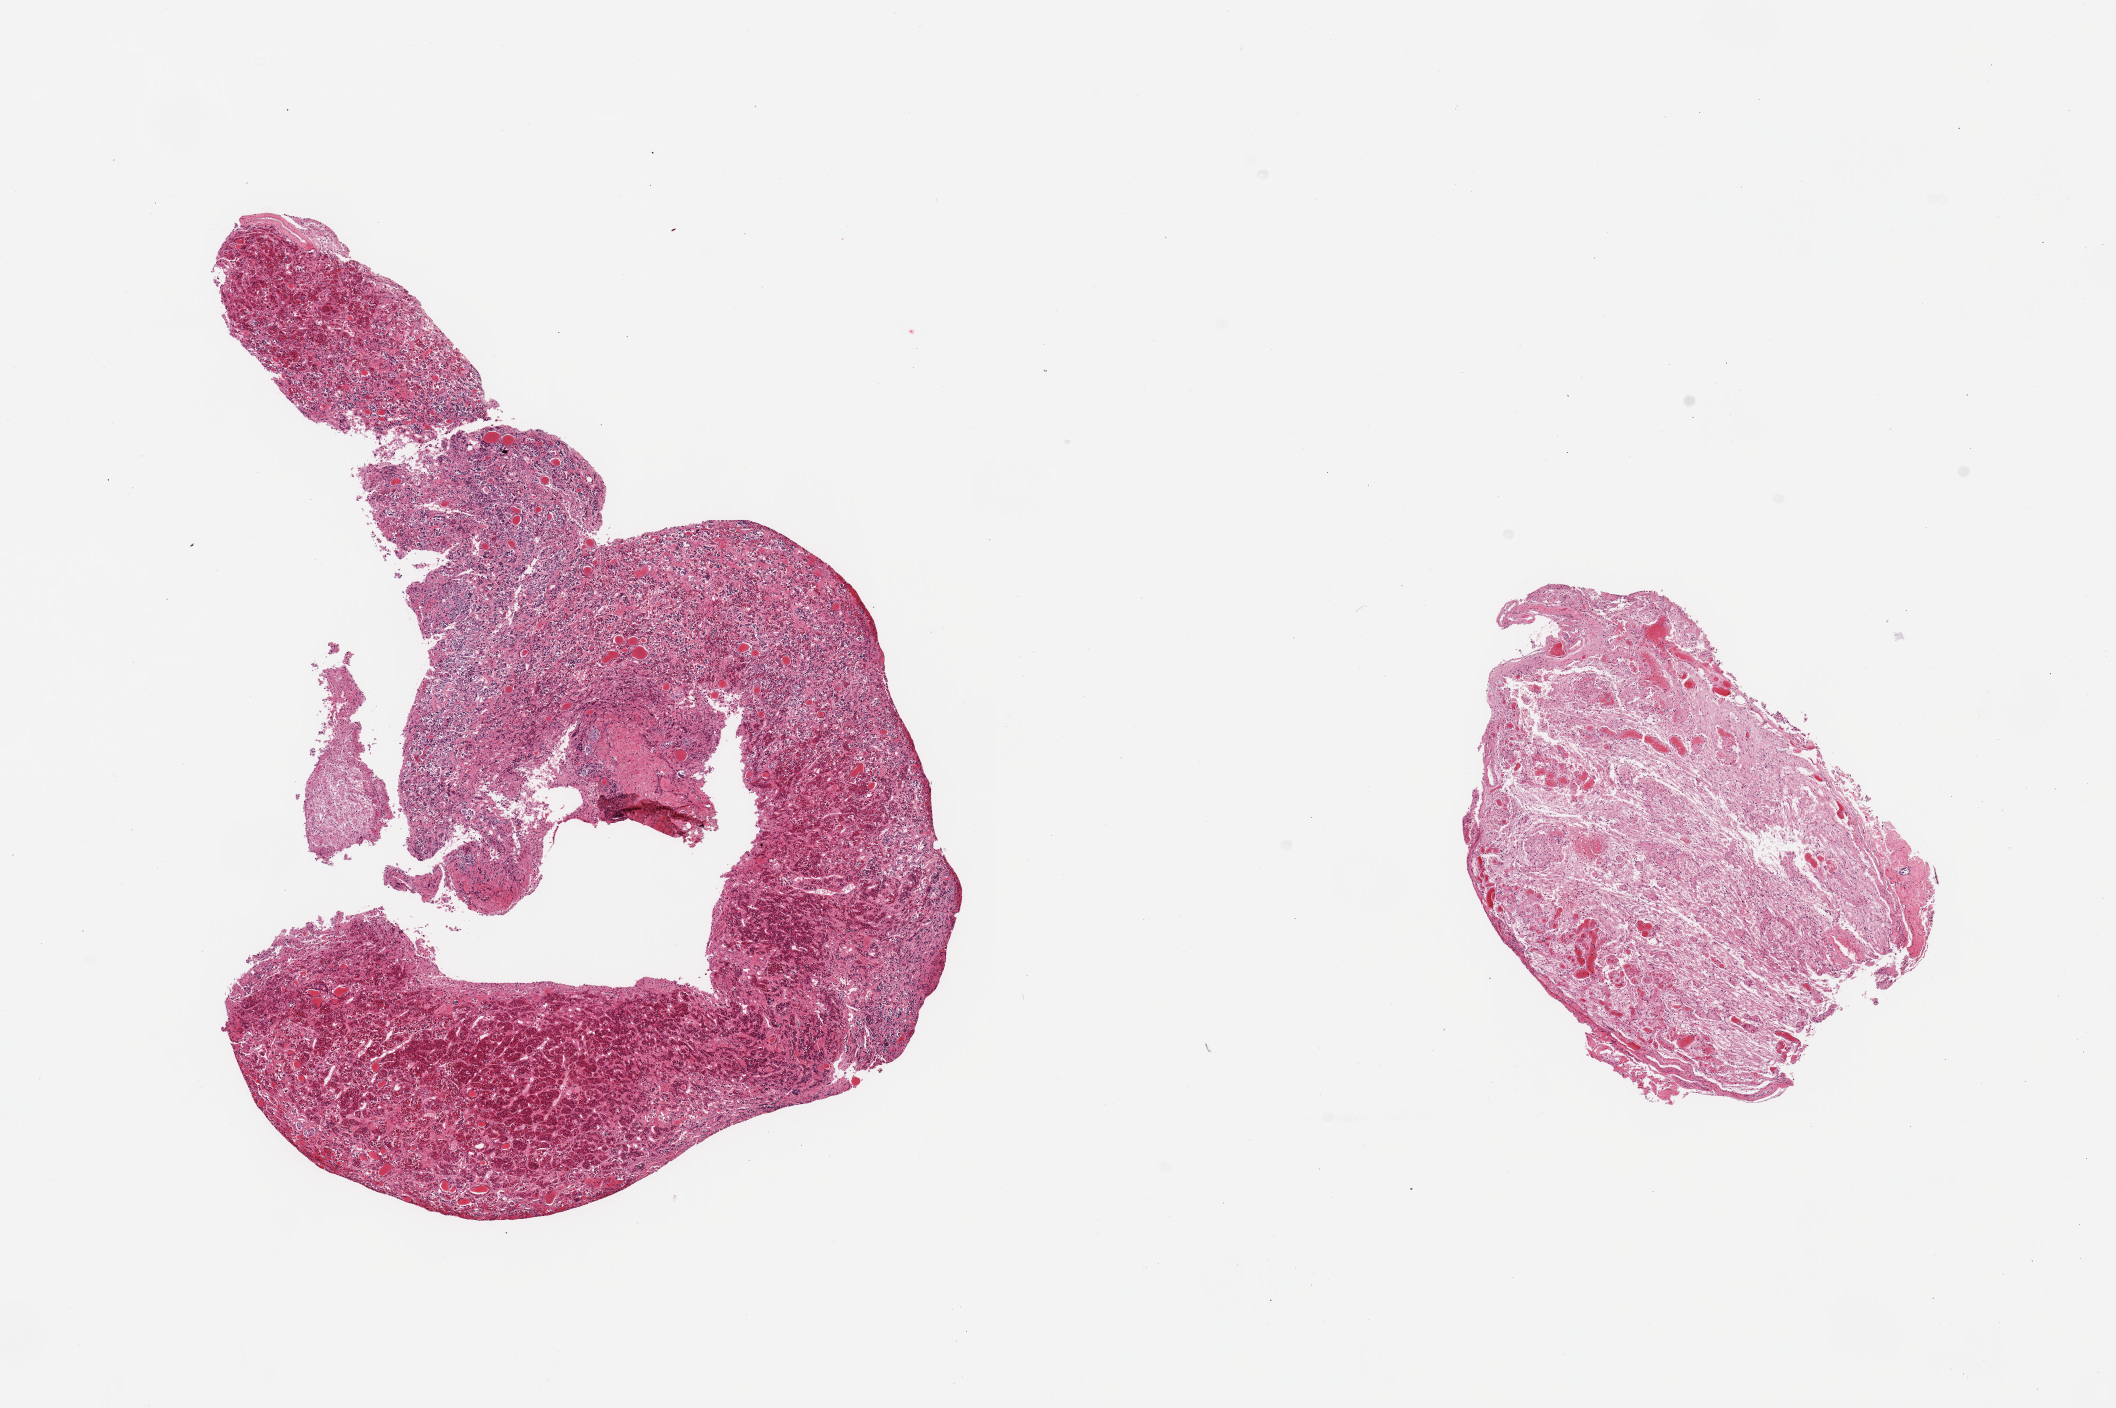
Hematoxylin and eosin (H&E) whole-slide image, shown as a low-resolution overview of the whole scanned area (about 16.7 x 11.1 mm, slide scanned at 20x). PAXgene-fixed paraffin-embedded (PFPE) section. Sampled site (target tissue): pituitary. Tissue donor sample. Donor sex: female.
- review note (as recorded): 2 pieces: 1 is anterior with small piece of posterior; other is all posterior